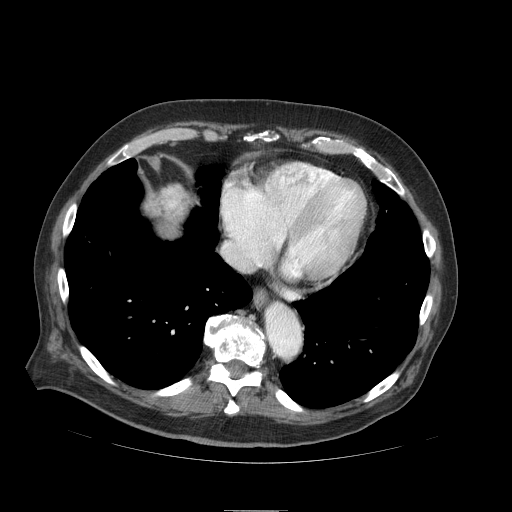
Contrast-enhanced abdominal CT (liver protocol), one axial slice. Position 87 of 103 along the scan axis. Reconstruction kernel STANDARD. 120 kVp. Soft-tissue window (W 400 / L 40 HU). 2.5 mm slice thickness. 512 × 512 image matrix, field of view 440 × 440 mm. From the clinical record (not read from this slice): diagnosis: hepatocellular carcinoma (patient treated with transarterial chemoembolisation; whether this scan precedes or follows treatment is not stated here); TNM stage (as recorded): Stage-IIIA; Child-Pugh class: B; tumour differentiation: well differentiated.
Structures marked on this image (semi-automatically segmented with operator editing):
- mass: bounding box (x1, y1, x2, y2) in pixels: (144, 183, 195, 238)